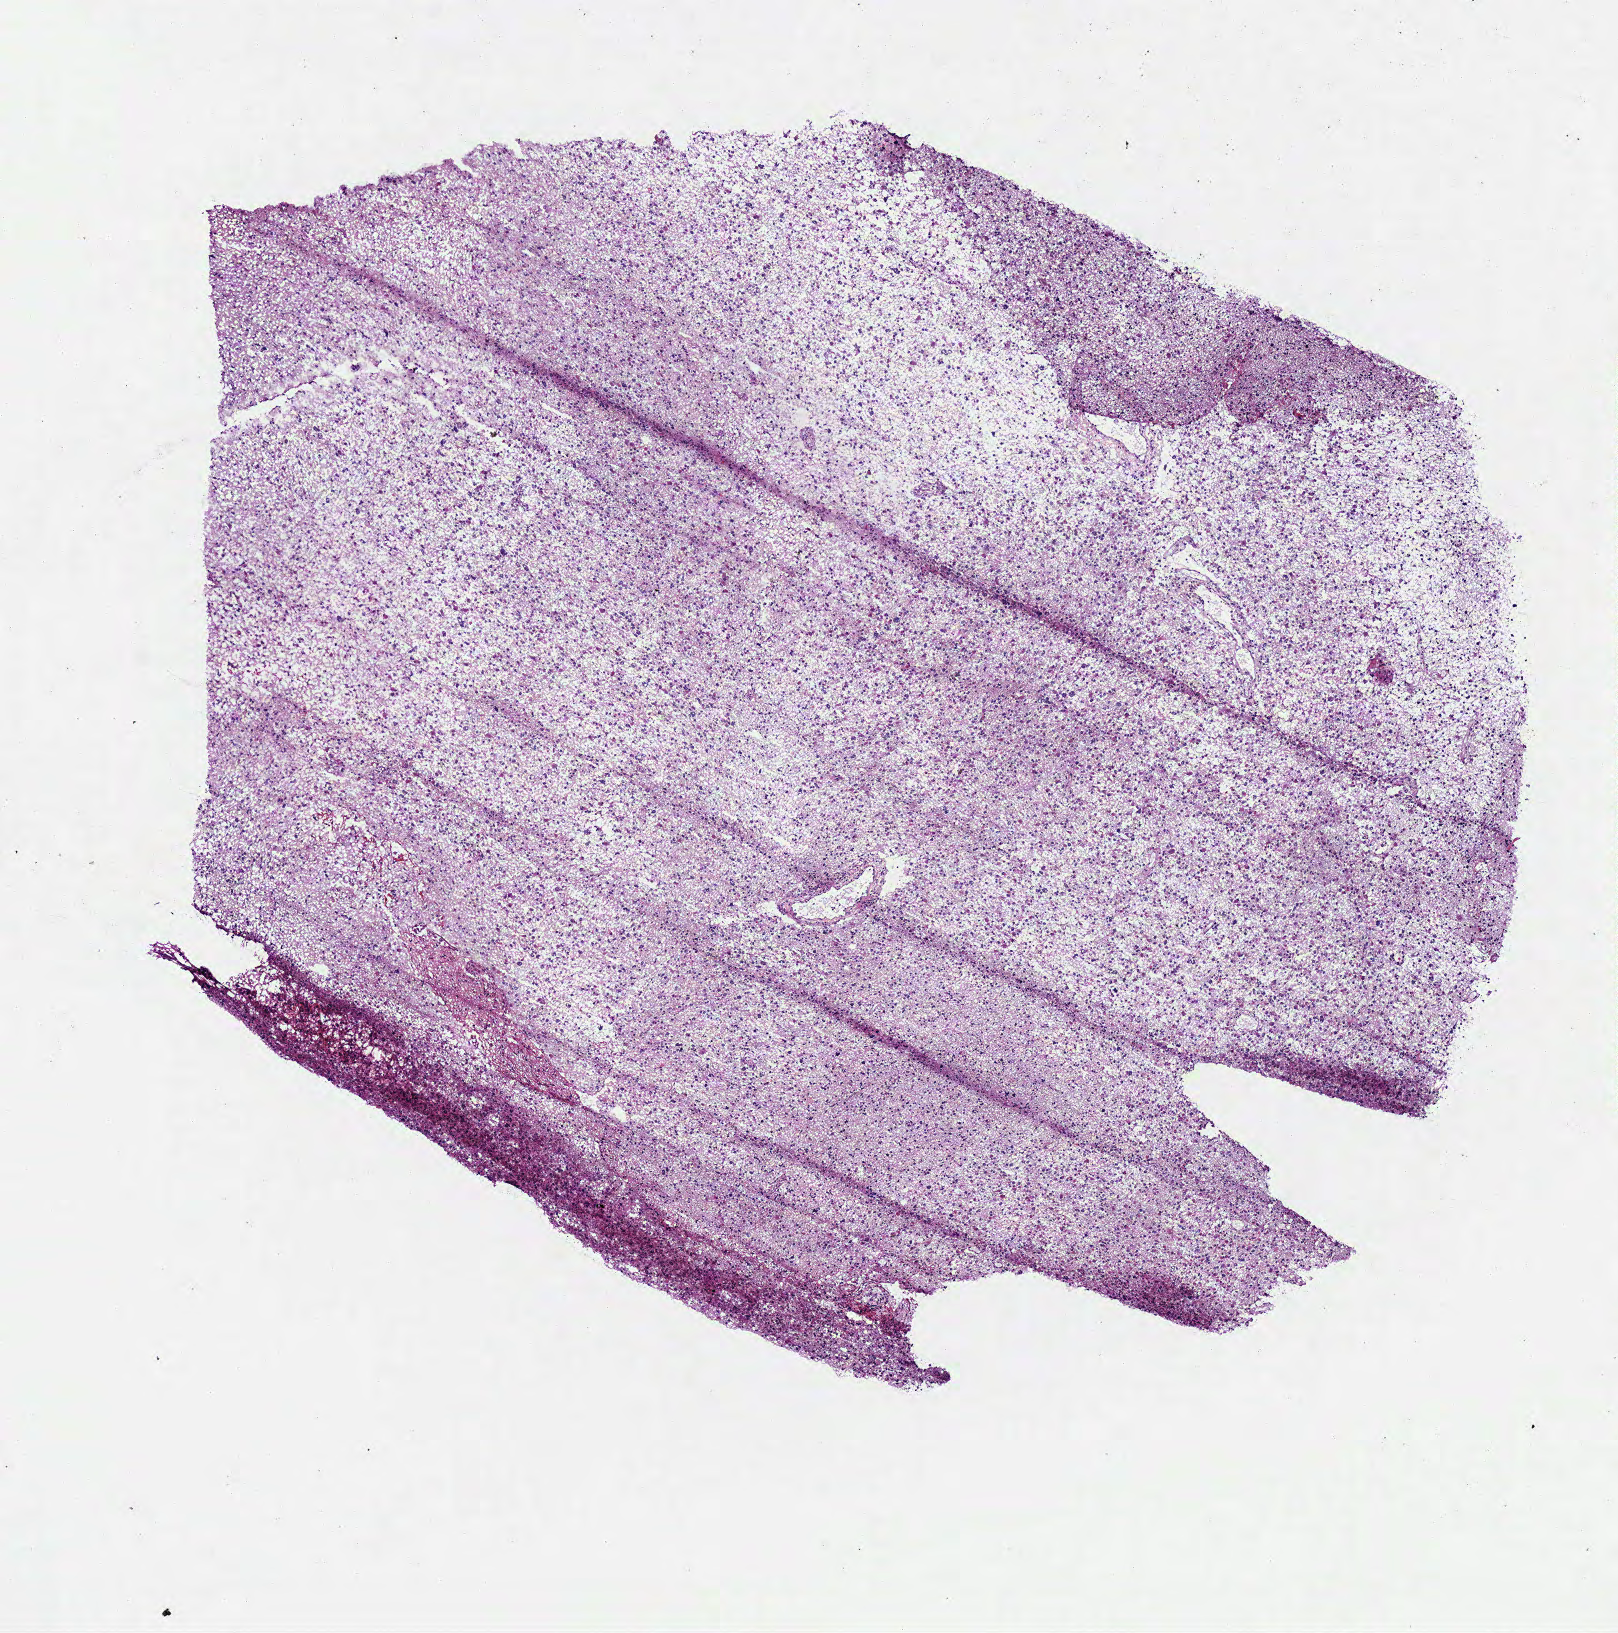
H&E whole-slide image — a low-resolution overview of the entire scanned area, about 6.4 x 6.4 mm (from a 40x scan); frozen section; sample: primary tumour, brain. Female, age 49 years at initial diagnosis. Slide review estimates, as recorded: tumour cells 100%, tumour nuclei 80%, normal cells 0%, stromal cells 0%, necrosis 0%.
Pathologic diagnosis: Glioblastoma.